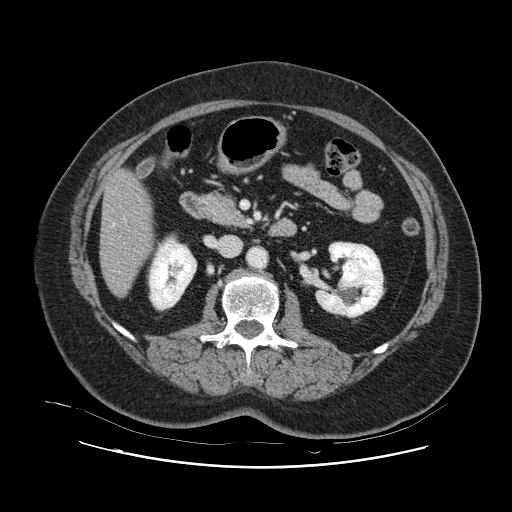
Contrast-enhanced abdominal CT, one axial slice; position 33 of 132 along the scan axis; 120 kVp; intravenous contrast given; soft-tissue window (W 400 / L 40 HU); 2.5 mm slice thickness; 512 × 512 image matrix, field of view 391 × 391 mm. Female patient, age 73 years. Case-level facts recorded for this patient, not image findings: diagnosis: colorectal cancer liver metastases, imaged before liver resection; multiple liver metastases: no; largest metastasis: 7 cm; disease in both lobes: no.
Annotated regions visible in this slice (manually delineated by an expert):
- hepatic veins: bounding box (x1, y1, x2, y2) in pixels: (112, 223, 115, 226)
- liver: (101, 172, 152, 297)
- planned liver remnant (the part of the liver to remain after resection): (101, 171, 152, 297)